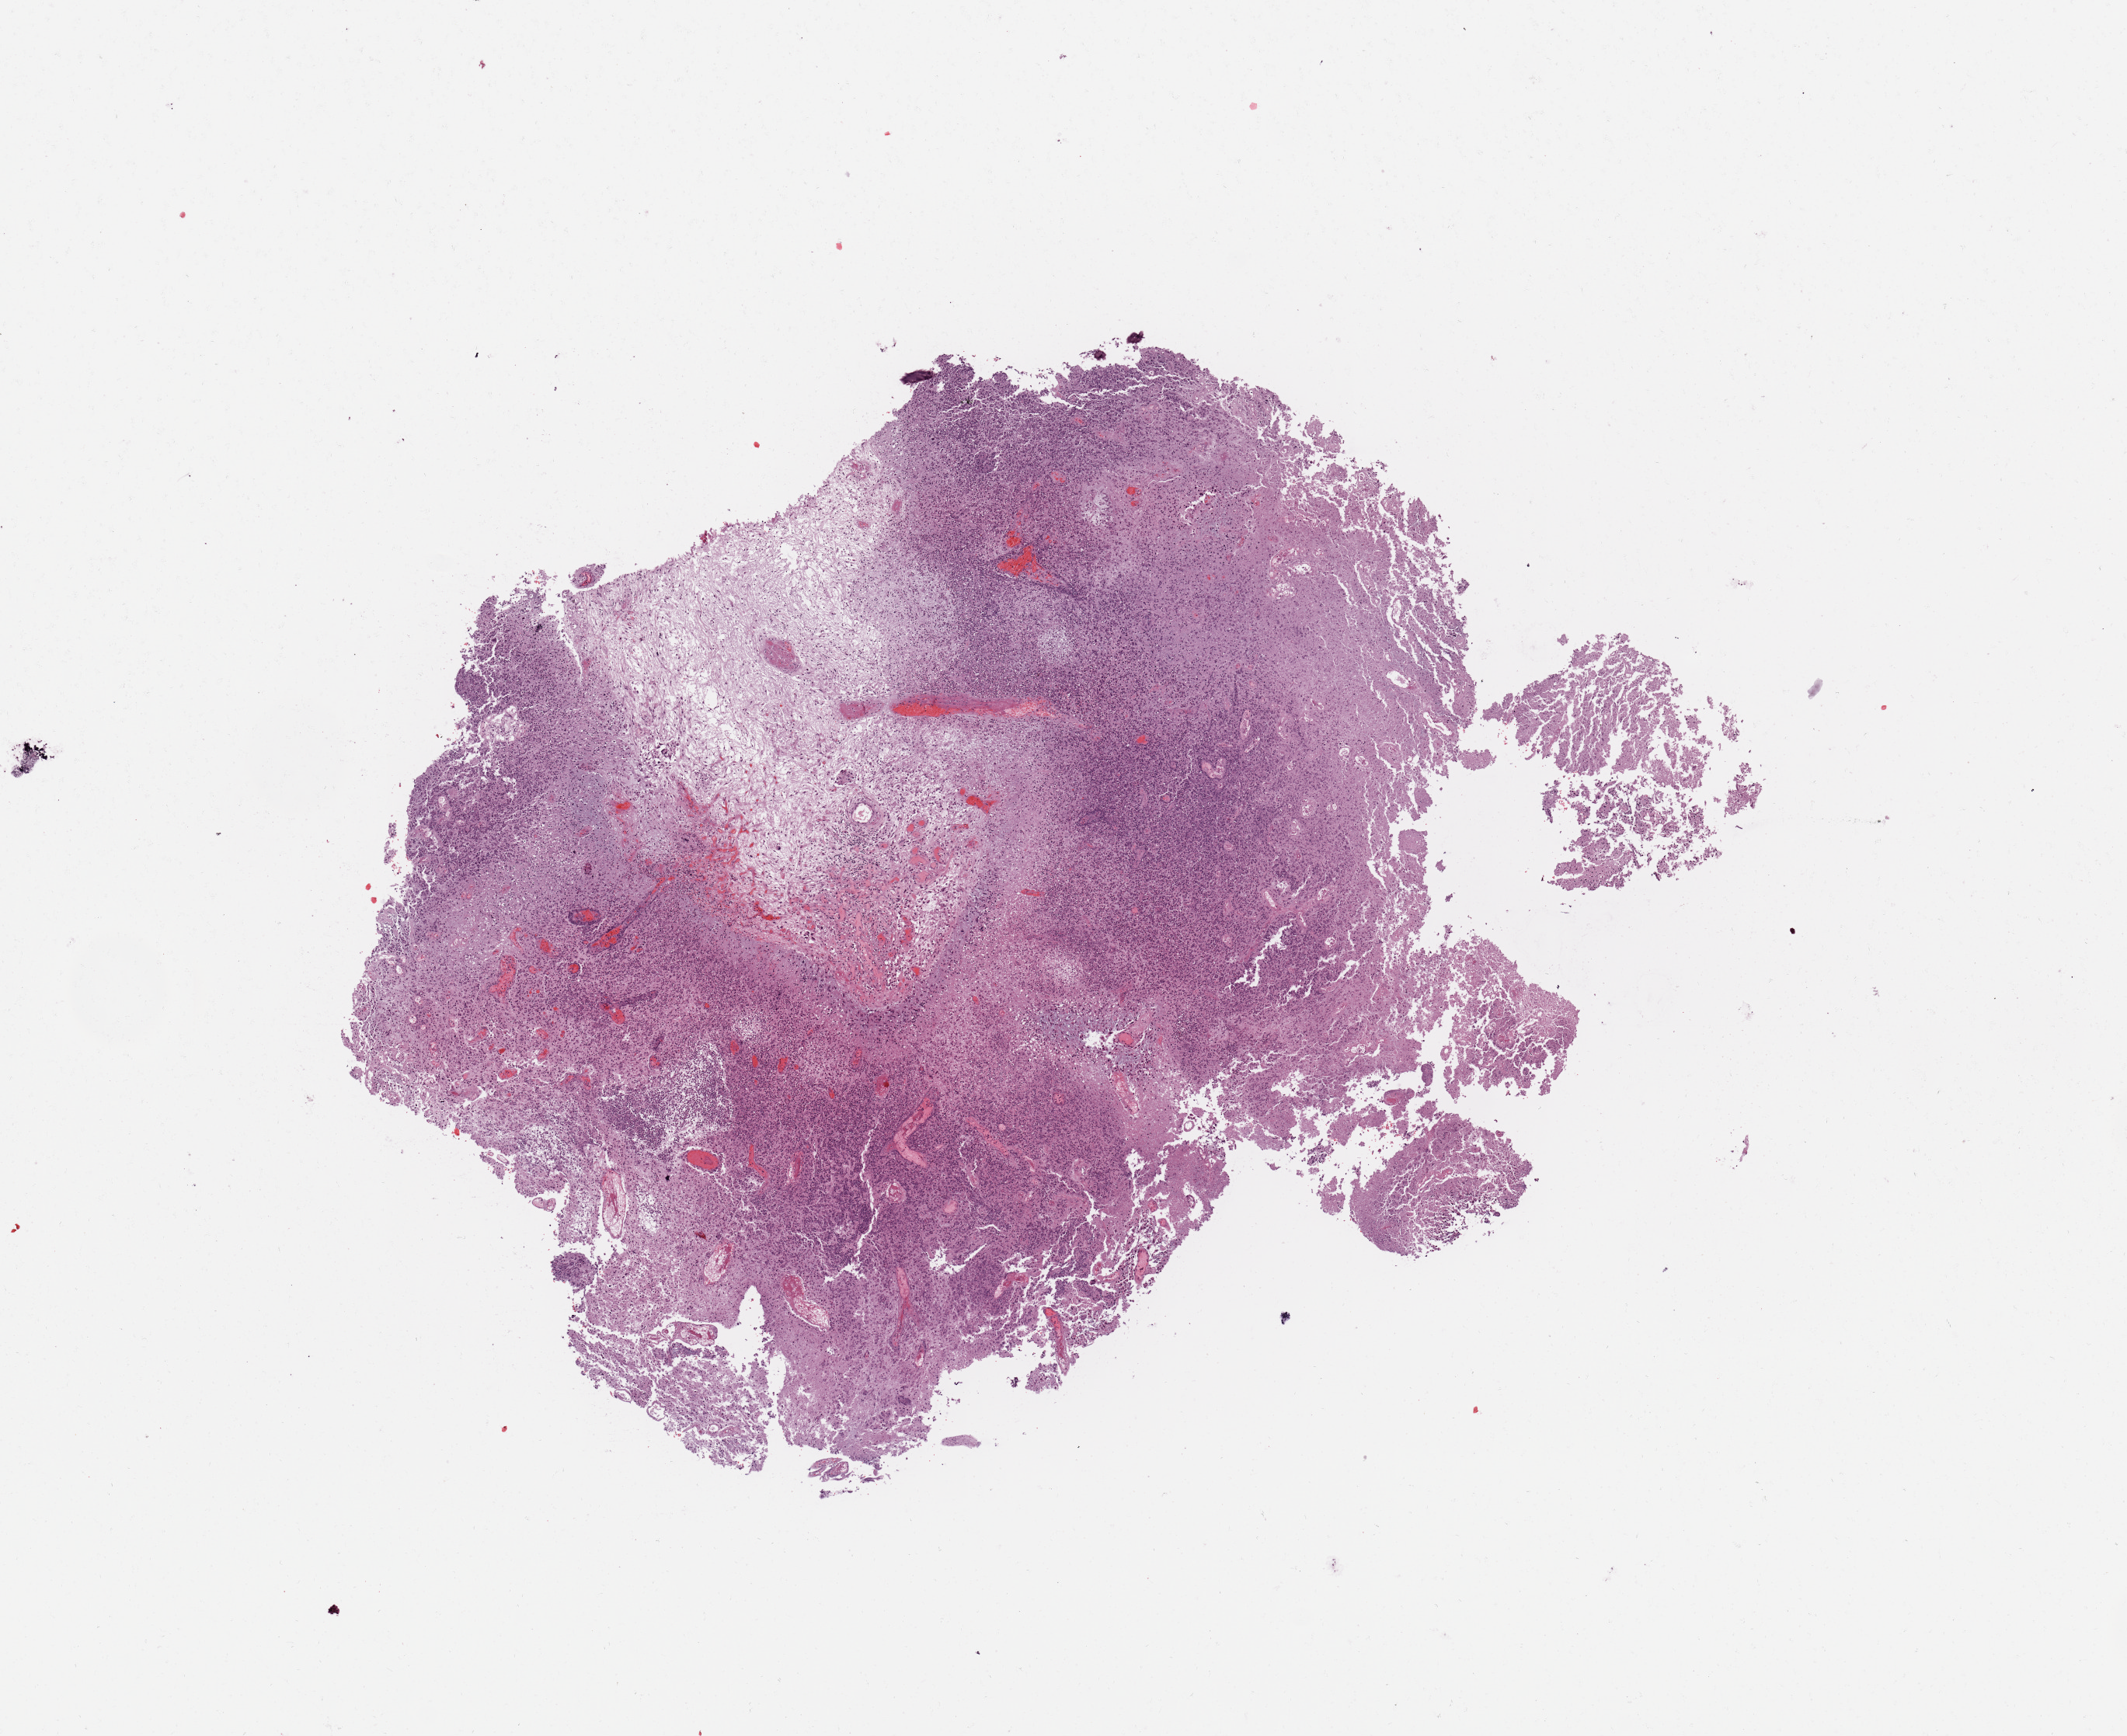
Whole-slide histology image, H&E-stained — a low-resolution overview of the entire scanned area, about 10.8 x 8.8 mm. Tumour tissue sample, brain. Patient: female, age 72 years.
* primary tumour site (as recorded): temporal lobe
* histologic diagnosis: Glioblastoma